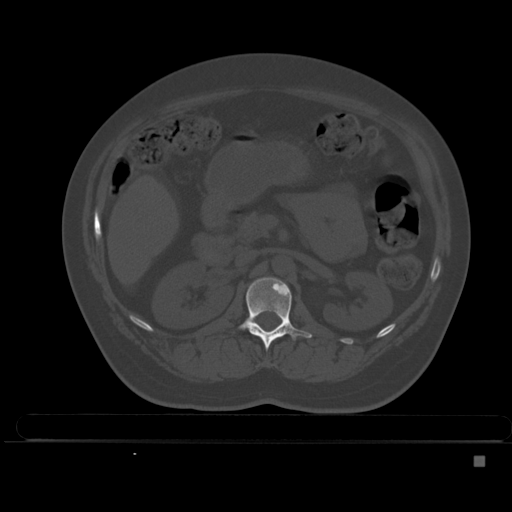
CT including the spine, one axial slice; position 193 of 495 along the scan axis; bone window (W 1800 / L 400 HU); 512 × 512 image matrix. Patient: female, 33 years. Case-level facts recorded for this patient, not image findings: primary cancer: breast.
Annotated regions visible in this slice (semi-automatically segmented with operator editing):
- L1 vertebra: bounding box (x1, y1, x2, y2) in pixels: (238, 277, 312, 349)